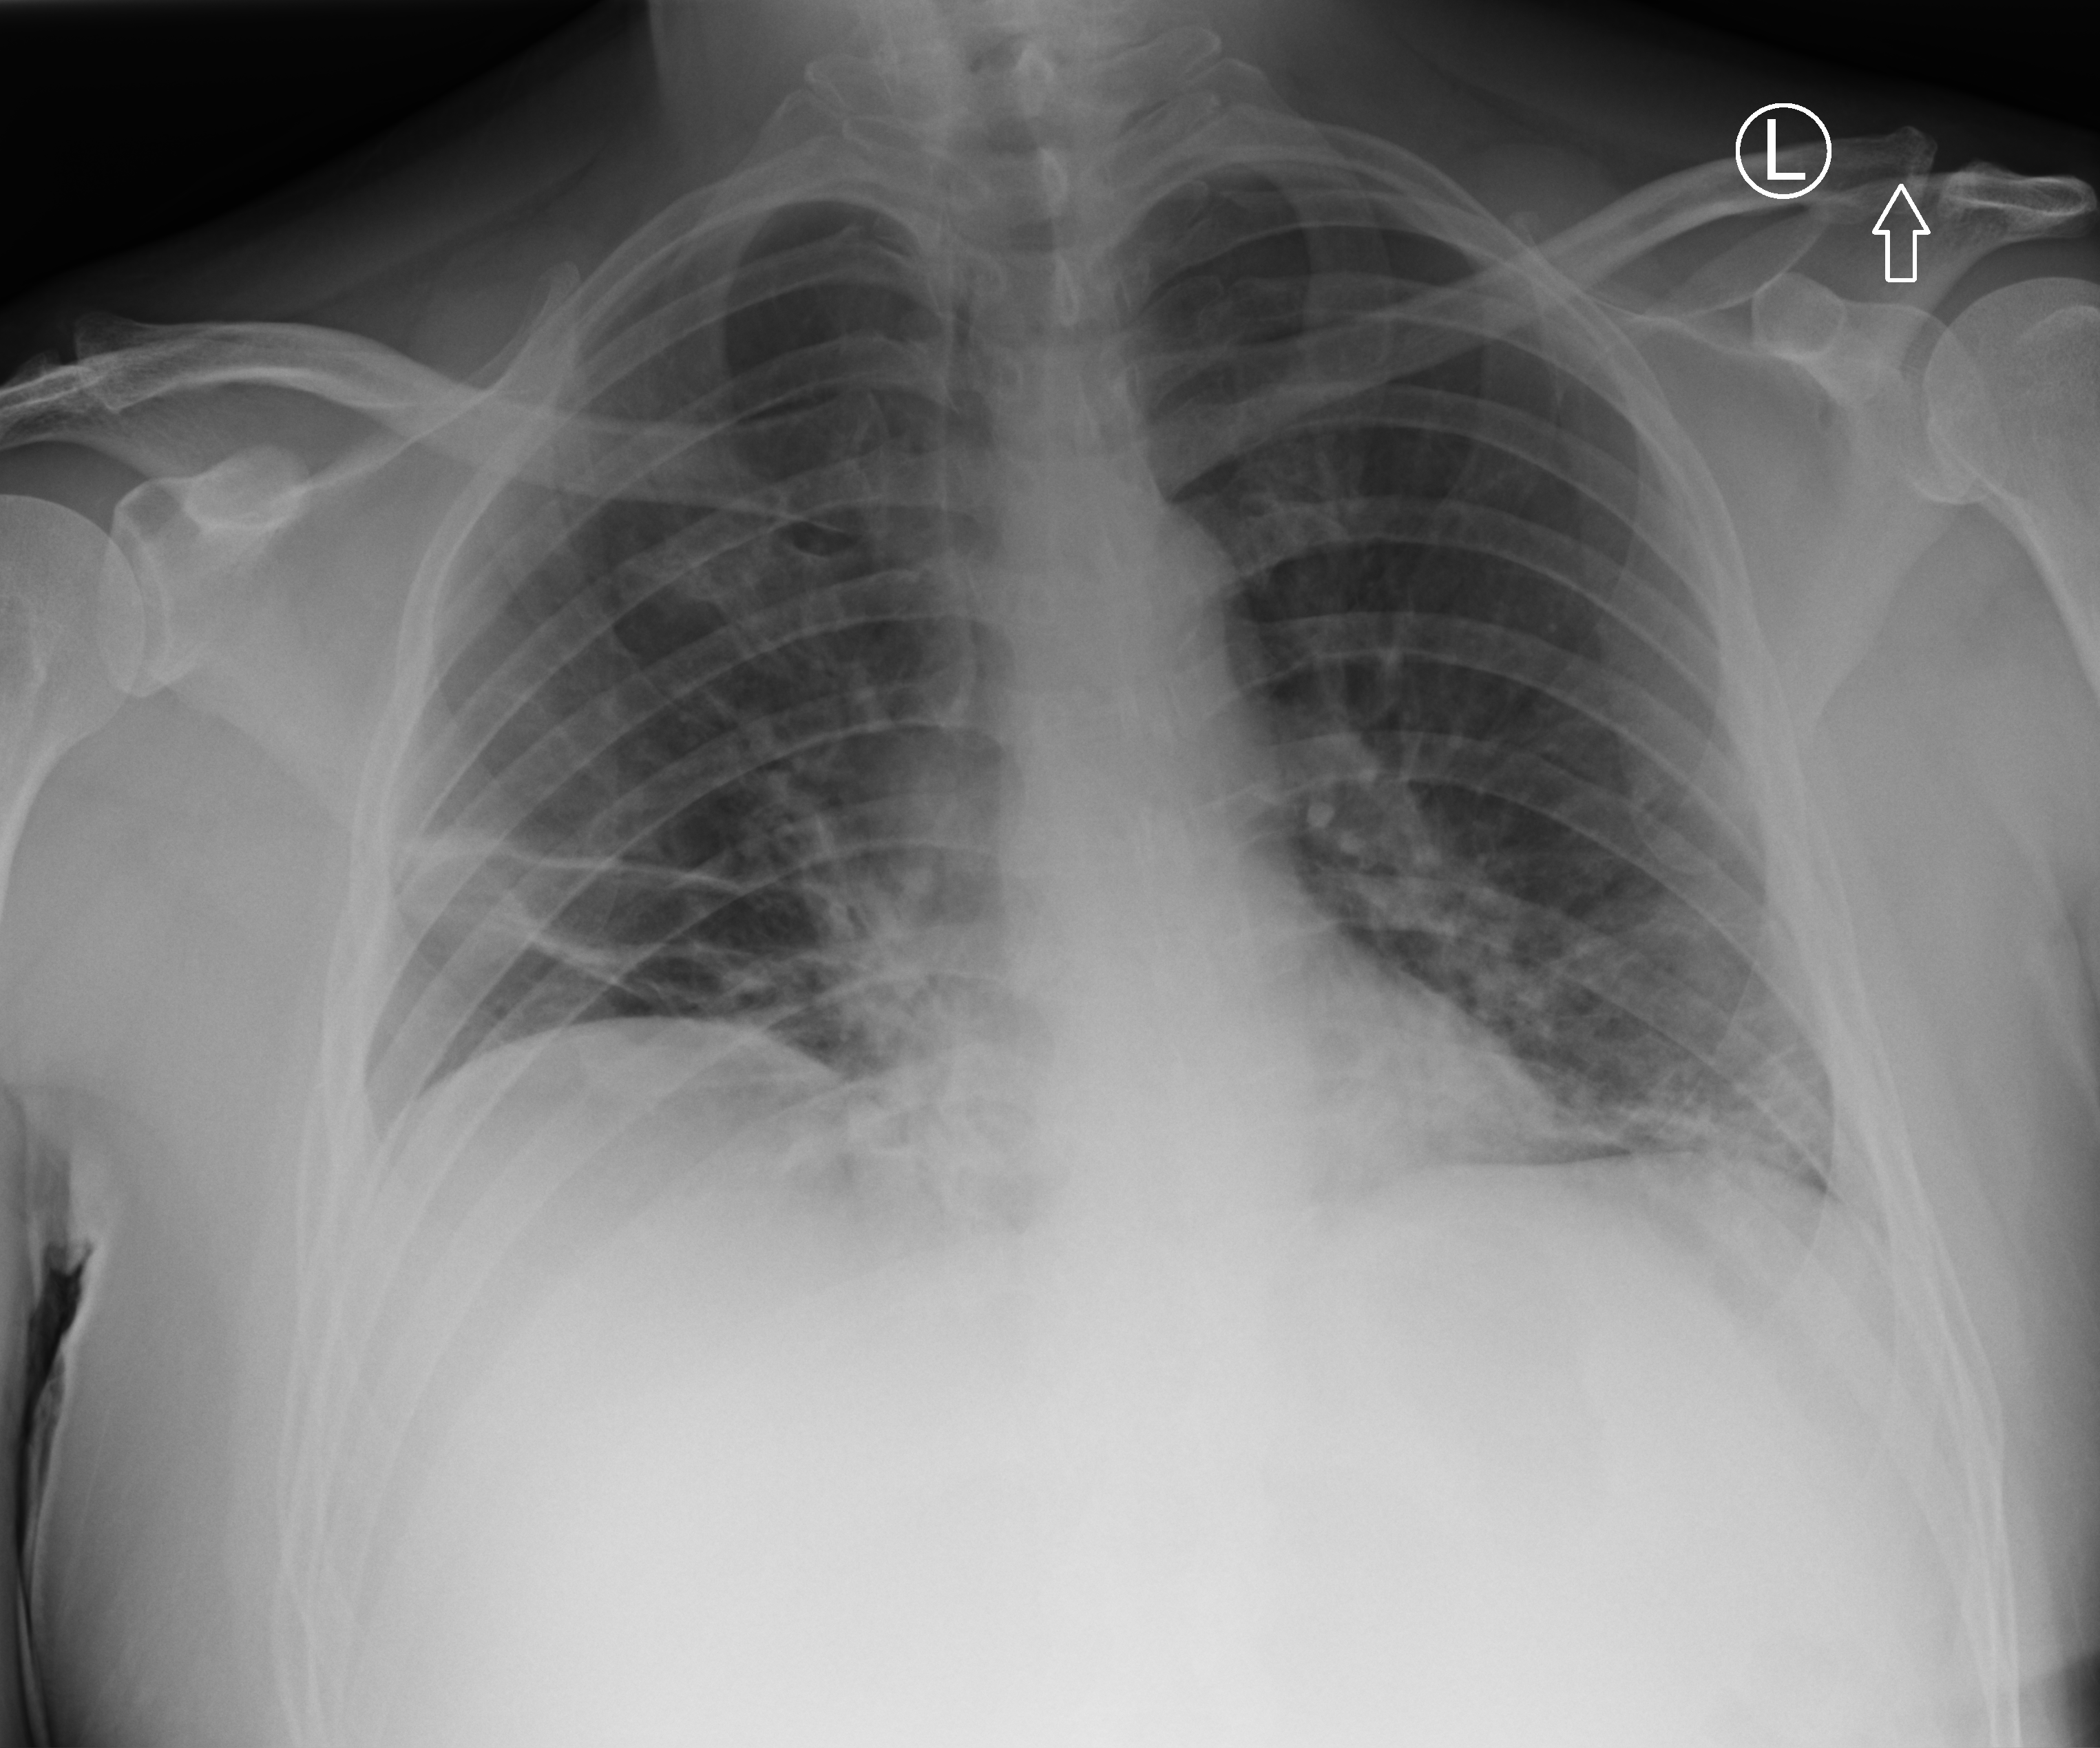
Portable chest radiograph; anteroposterior (AP) projection. Patient hospitalised with COVID-19; male, aged 18–59 years.
From the hospital-stay record, not from the radiograph (when in the stay this image was taken is not recorded):
- admitted to intensive care during this hospital stay: no
- mechanically ventilated during this hospital stay: no